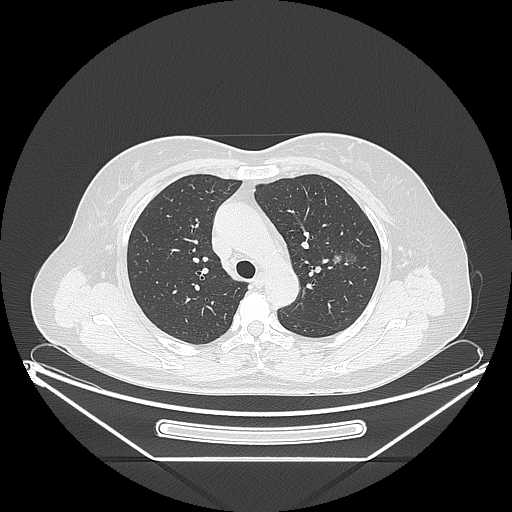
Chest CT, one axial slice; slice 152 of 226 in the series (ordered by position); lung window (W 1500 / L -600 HU); 512 × 512 image matrix. Patient: female, 54 years. Case-level facts recorded for this patient, not image findings: clinical TNM (as recorded): T1c N0 M0; histopathological grade: G1.
Outlined on this slice (bounding box drawn by a radiologist):
- lung tumour (recorded histology: adenocarcinoma): bounding box <325,242,357,271> (left, top, right, bottom; pixels)